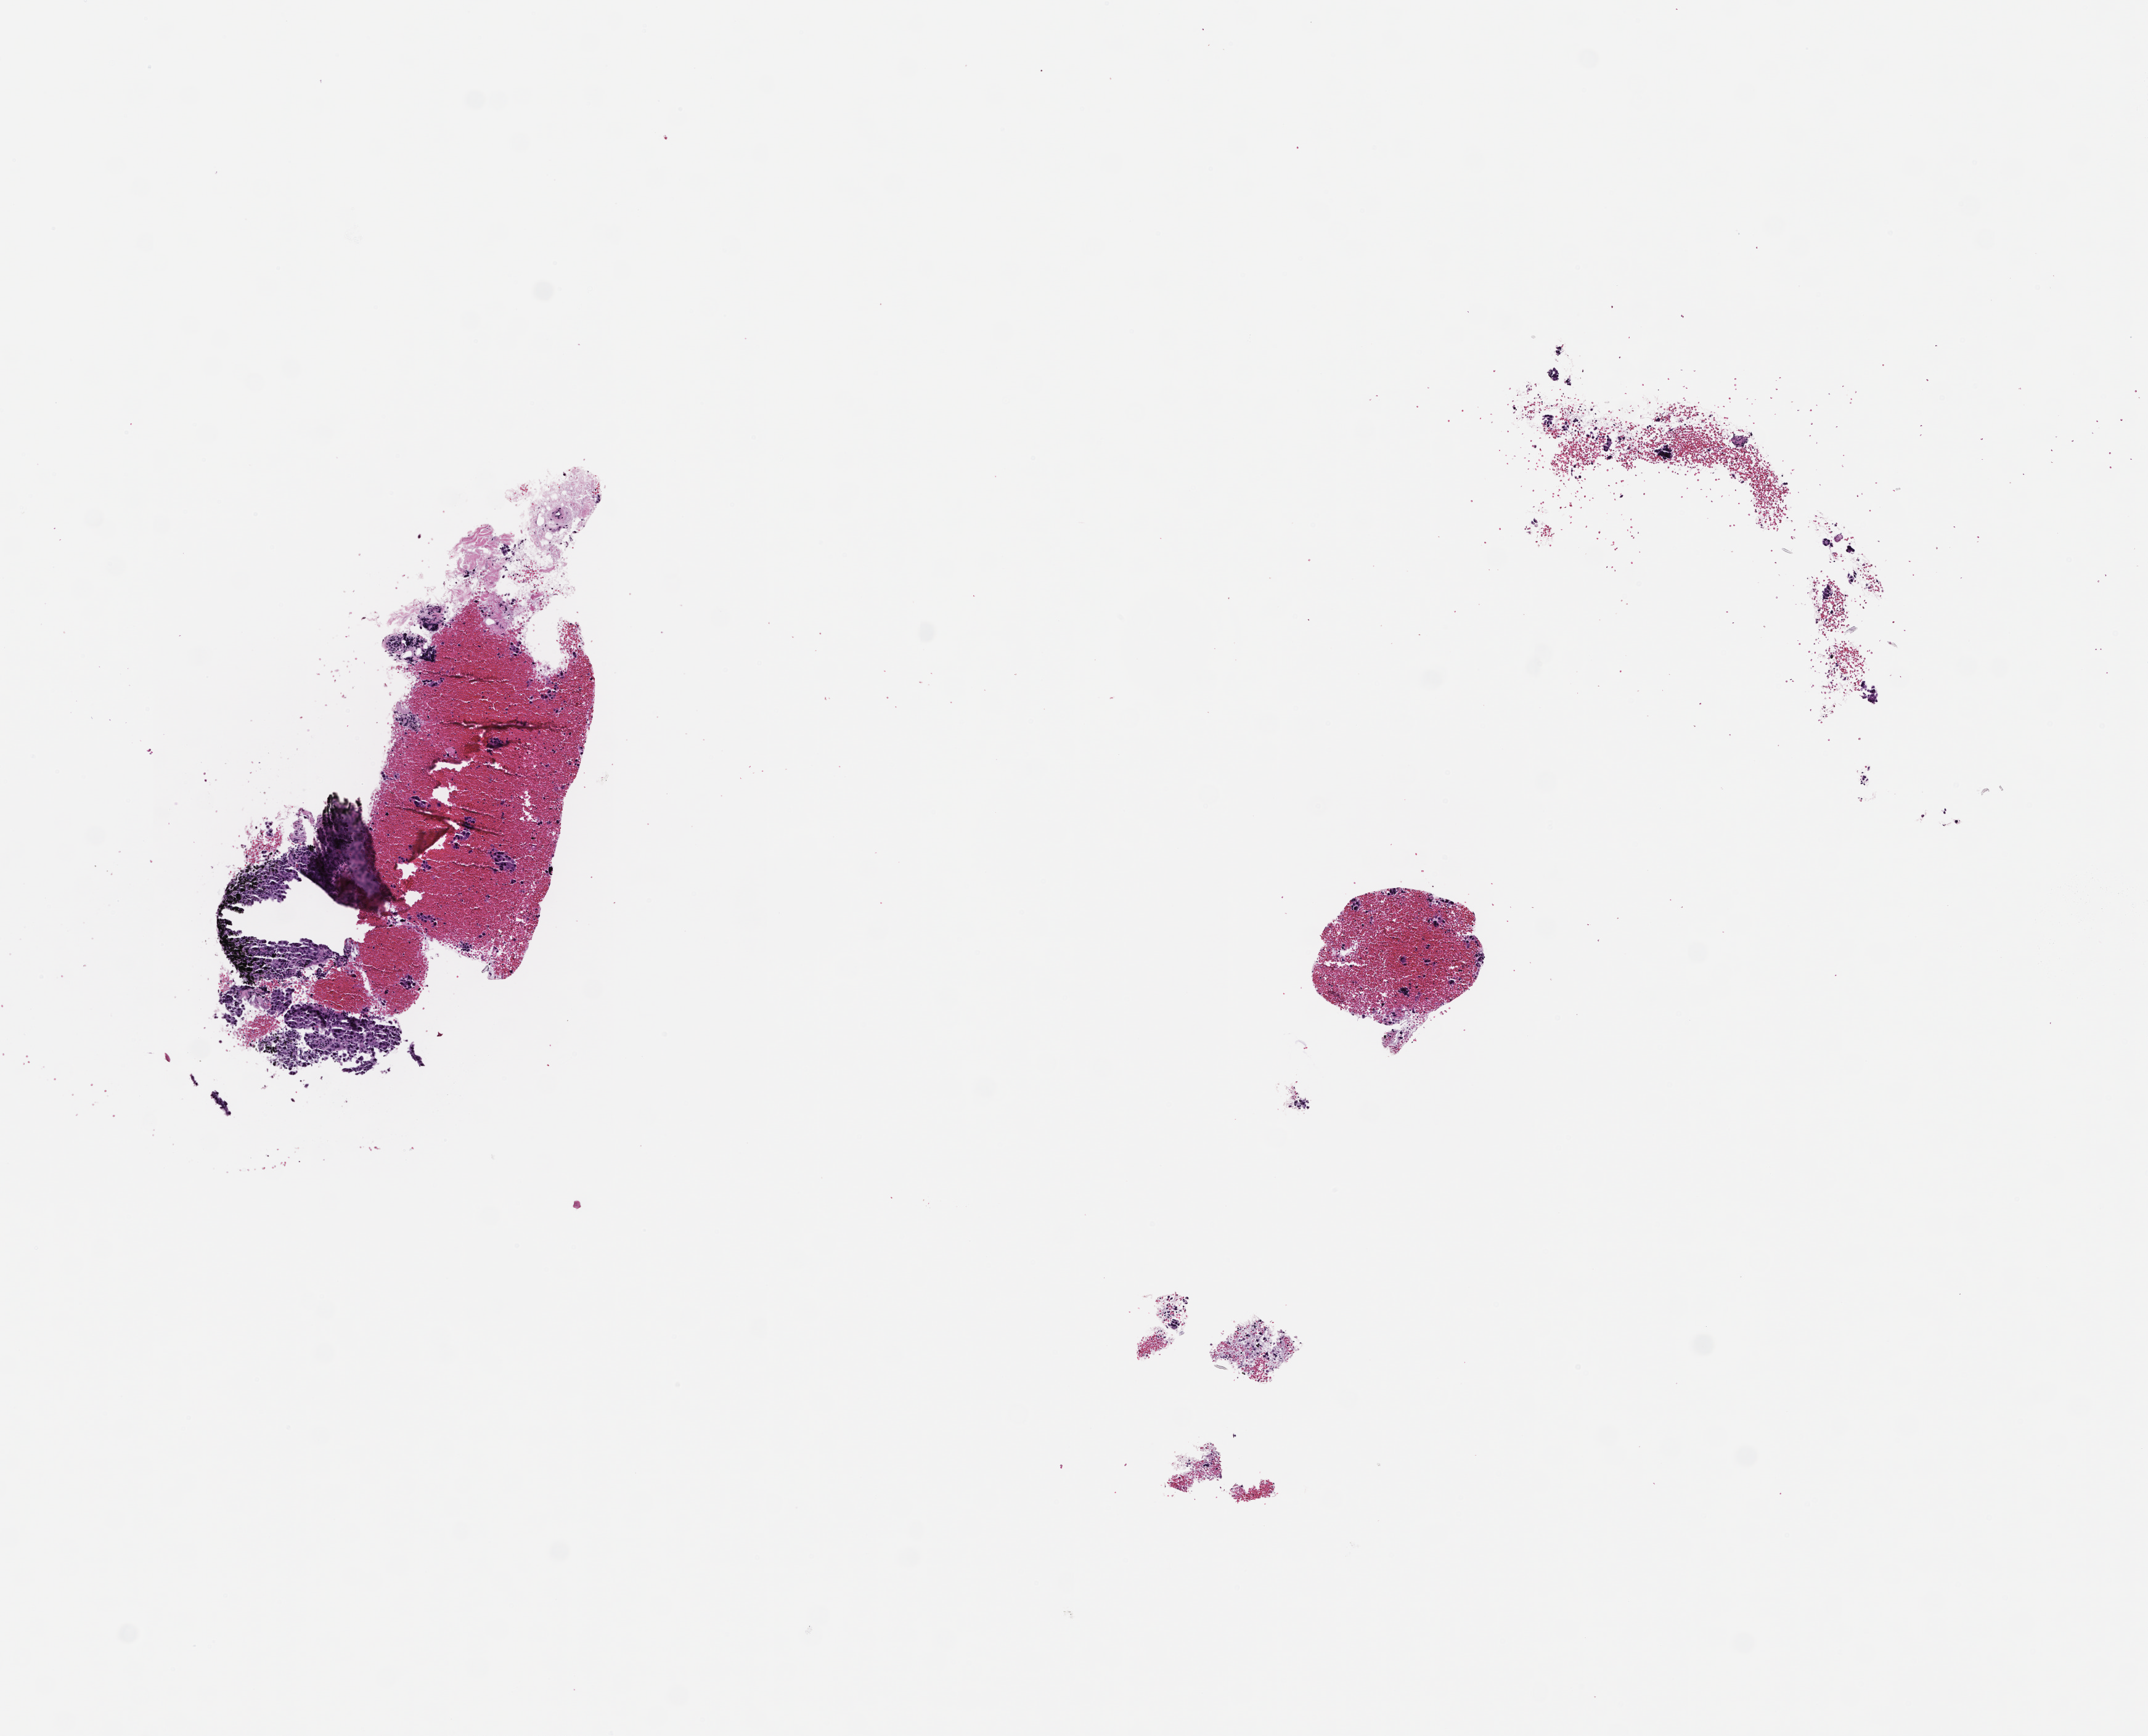
Digitized hematoxylin and eosin (H&E)-stained section, a low-resolution overview of the entire scanned area, about 7.0 x 5.7 mm; formalin-fixed, paraffin-embedded (FFPE) tissue; site: lung. Female patient.
This section: primary tumour tissue. Diagnosis: Non-Small Cell Lung Carcinoma.